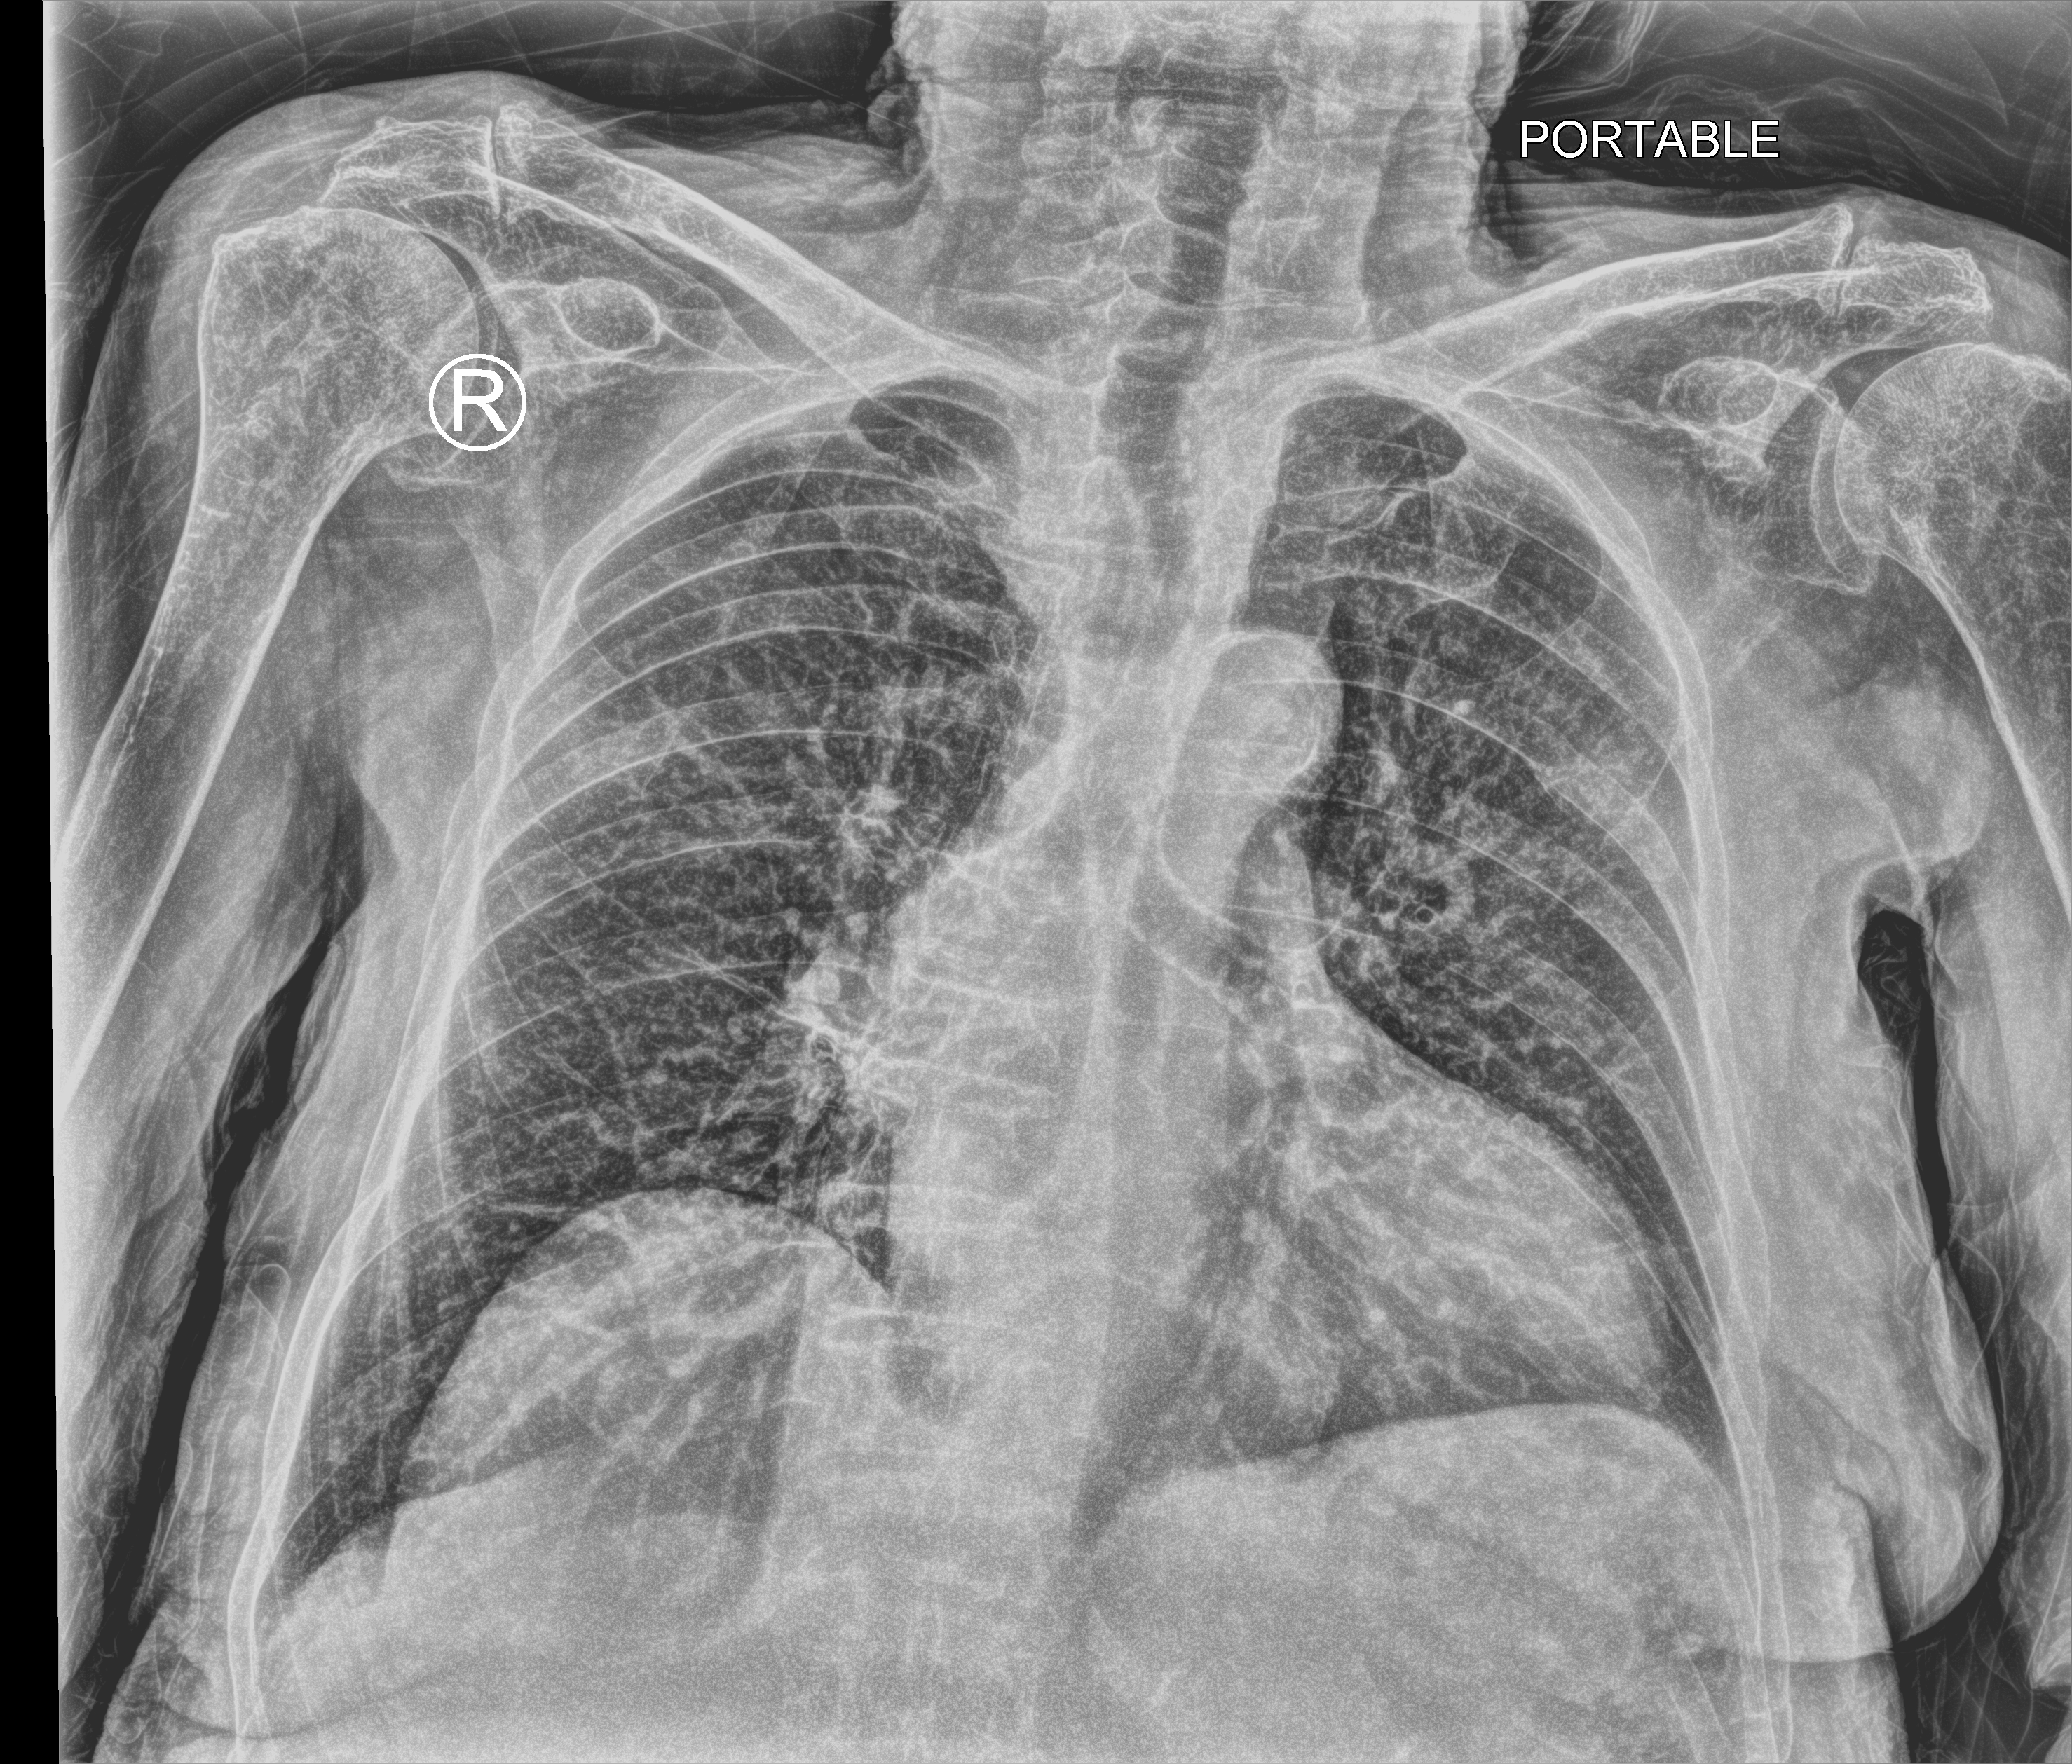
Portable chest radiograph. Female patient hospitalised with COVID-19, age 75–90 years.
Admission-level facts for this patient (not findings on this image; timing relative to this image not recorded):
- length of hospital stay: 8 days